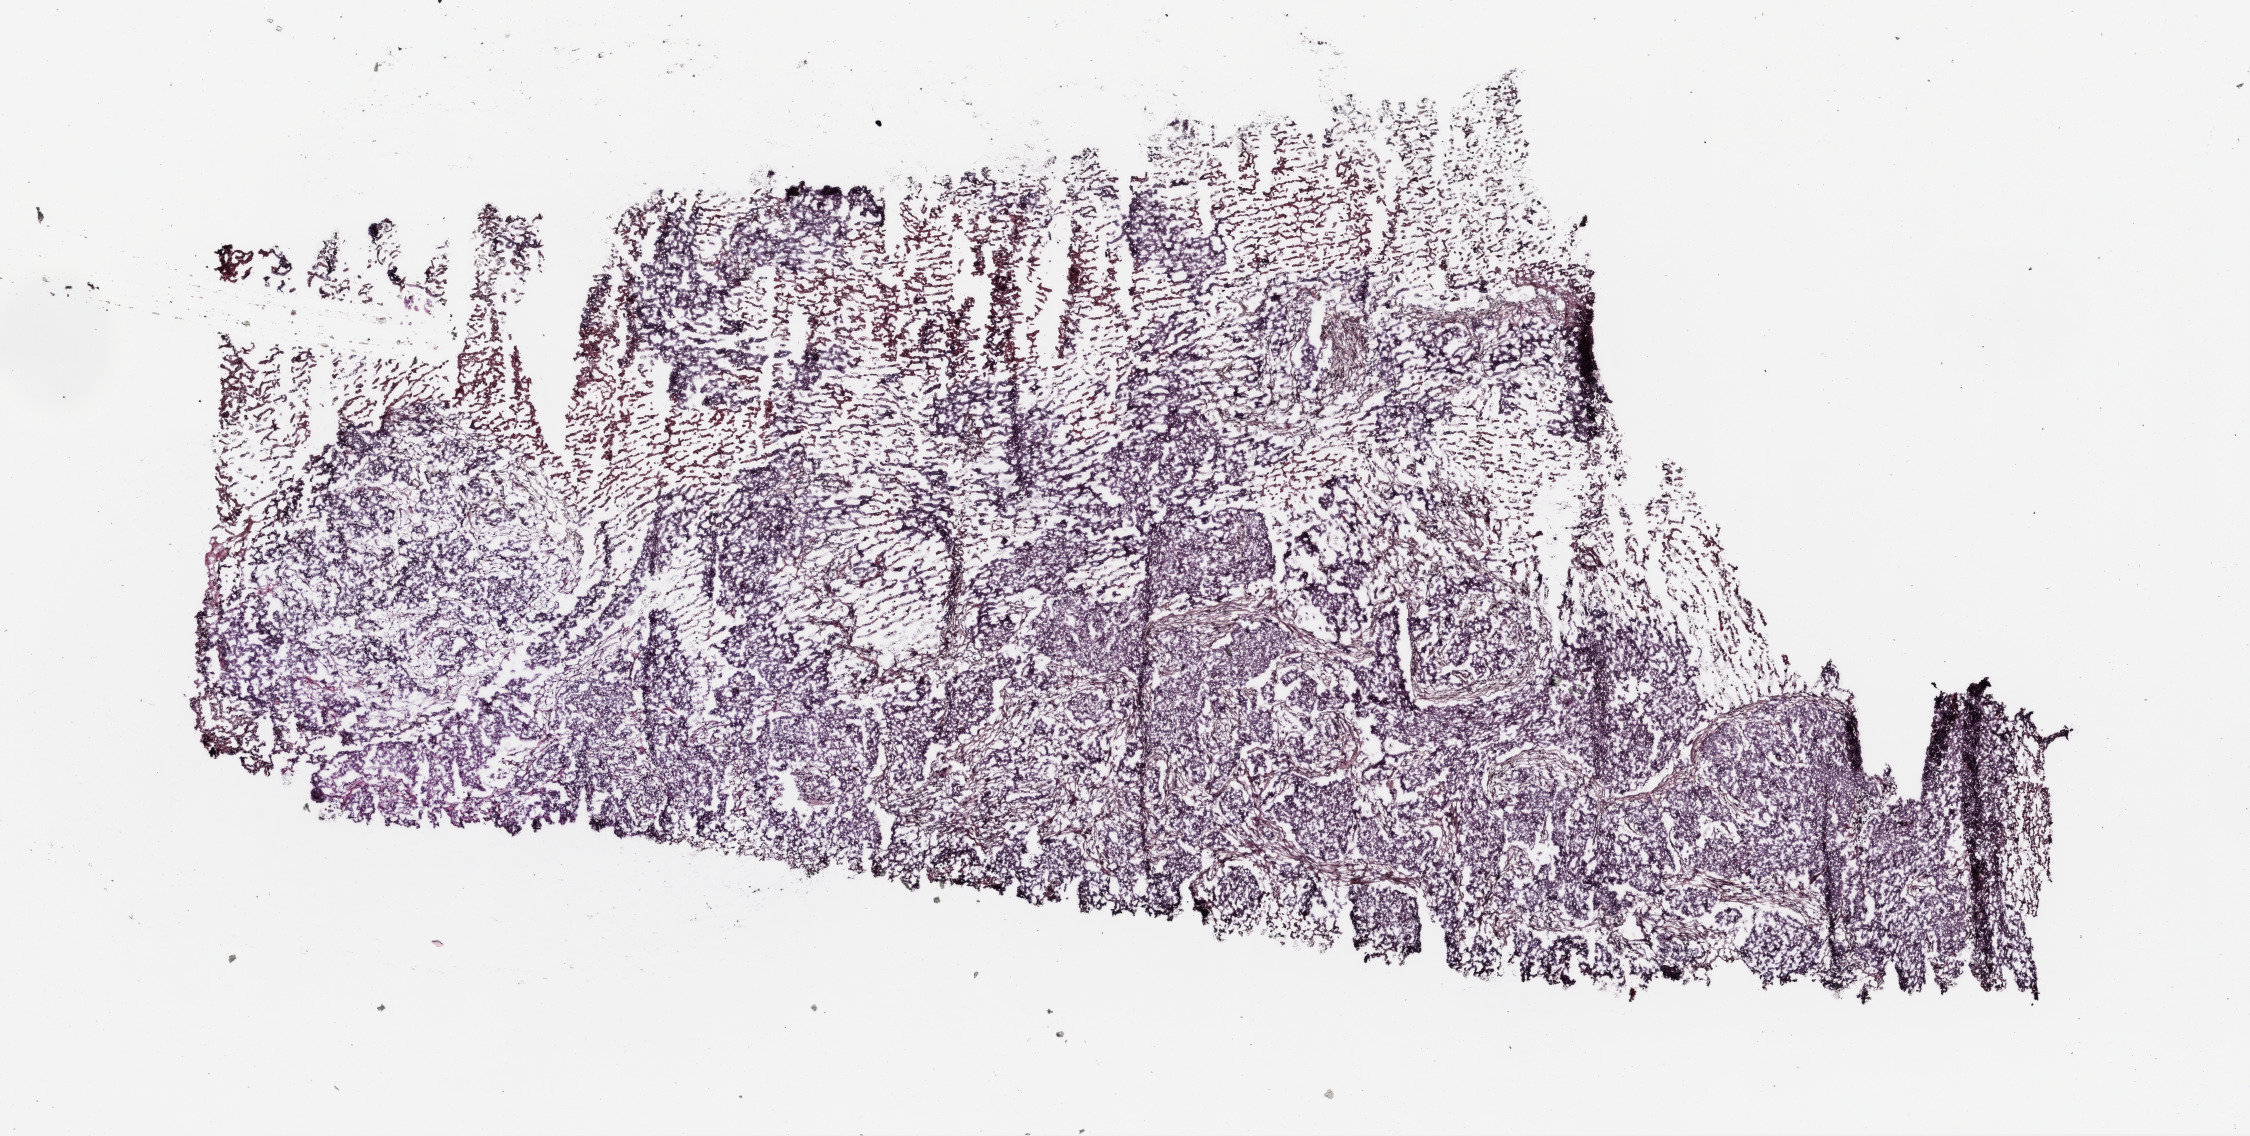
Whole-slide histology image, Hematoxylin and eosin (H&E) stained, a low-resolution overview of the entire scanned area, about 9.0 x 4.6 mm; frozen section from the top of the tissue portion; primary tumour sample from the lung. Female patient; age at initial diagnosis 75 years. Composition of this section per pathologist review: tumour cells 80%, tumour nuclei 80%, normal cells 0%, stromal cells 10%, necrosis 10%.
- laterality: right
- AJCC pathologic stage: IB (6th edition)
- diagnosis: Papillary adenocarcinoma, NOS (upper lobe, lung)